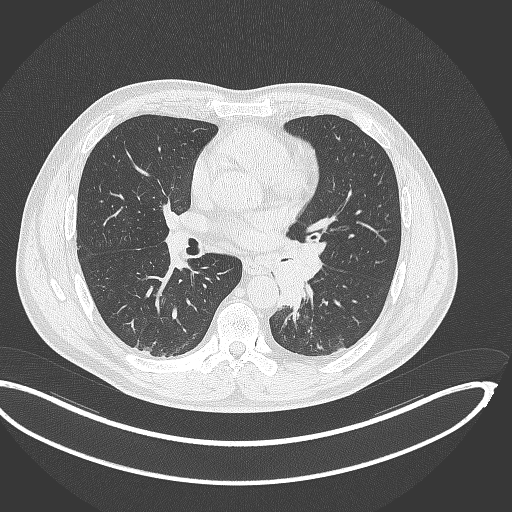
Chest CT, one axial slice; position 183 of 362 along the scan axis; reconstruction kernel B70f; 120 kVp; lung window (W 1500 / L -600 HU); 1 mm slice thickness; 512 × 512 image matrix, field of view 442 × 442 mm. Male patient, age 50 years. Case-level facts recorded for this patient, not image findings: clinical TNM (as recorded): T2a N3 M0.
Outlined on this slice (rectangle marked by the reading radiologist):
- lung tumour (recorded histology: squamous cell carcinoma): box from (x=267, y=249) to (x=323, y=313) px